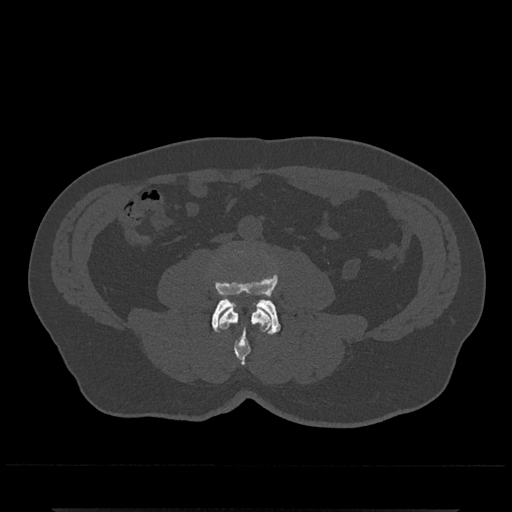
CT including the spine, one axial slice; slice 186 of 797 in the series (ordered by position); reconstruction kernel Br40s/3; 120 kVp; bone window (W 1800 / L 400 HU); 0.5 mm slice thickness; 512 × 512 image matrix, field of view 393 × 393 mm. Patient: male, 67 years. Case-level facts recorded for this patient, not image findings: primary cancer: prostate.
Structures marked on this image (semi-automatically segmented with operator editing):
- L3 vertebra: bounding box <218,306,272,365> (left, top, right, bottom; pixels)
- L4 vertebra: <212,276,281,334>